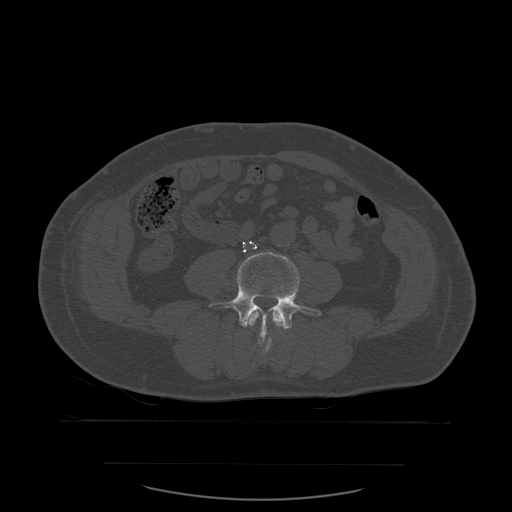
CT including the spine, one axial slice; bone window (W 1800 / L 400 HU); 512 × 512 image matrix, field of view 479 × 479 mm. Patient age 71 years. Case-level facts recorded for this patient, not image findings: primary cancer: lung; vertebrae with lytic lesions (as recorded): T1, T2, L5, S1.
Outlined on this slice (semi-automatic segmentation, software-assisted and operator-edited):
- L3 vertebra: bounding box <246,312,284,354> (left, top, right, bottom; pixels)
- L4 vertebra: <210,251,321,340>